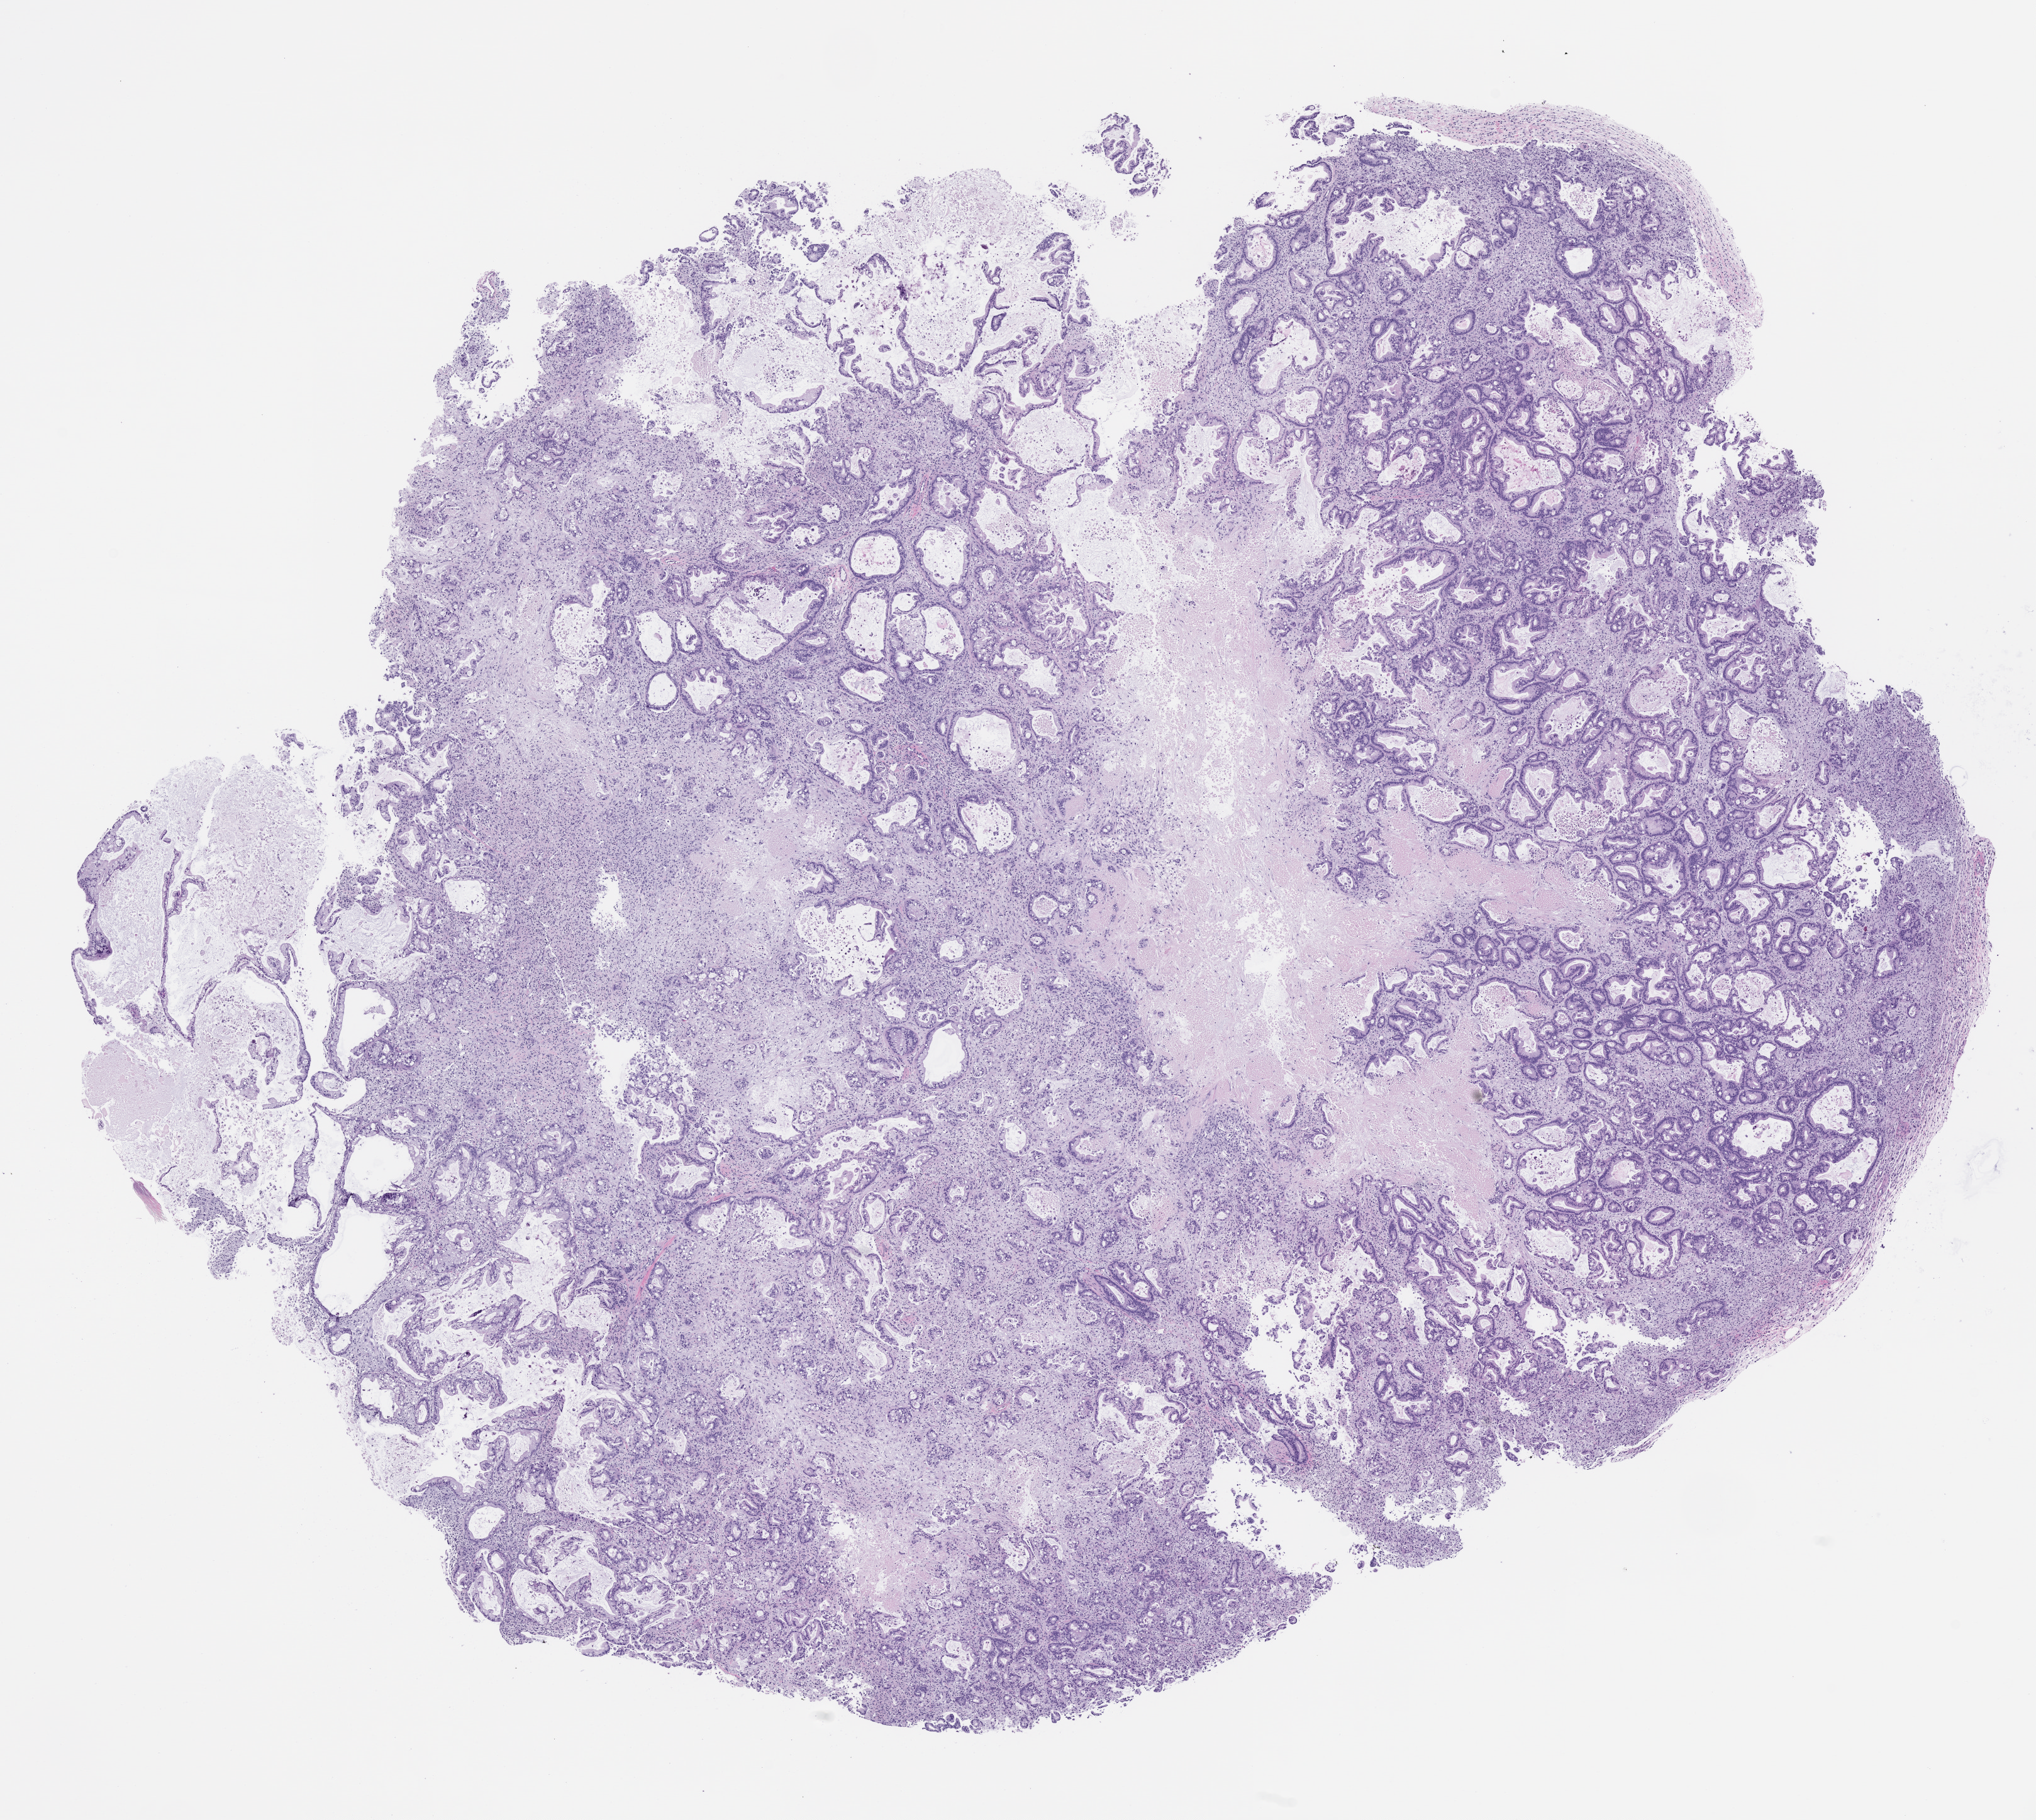
Hematoxylin and eosin (H&E) whole-slide image of a patient-derived xenograft (PDX) tumor grown in a mouse, passage 1, shown as a low-resolution overview of the whole scanned area (about 13.0 x 11.6 mm); FFPE section; tumor site category: pancreas.
Originating patient diagnosis: Pancreatic Adenocarcinoma.